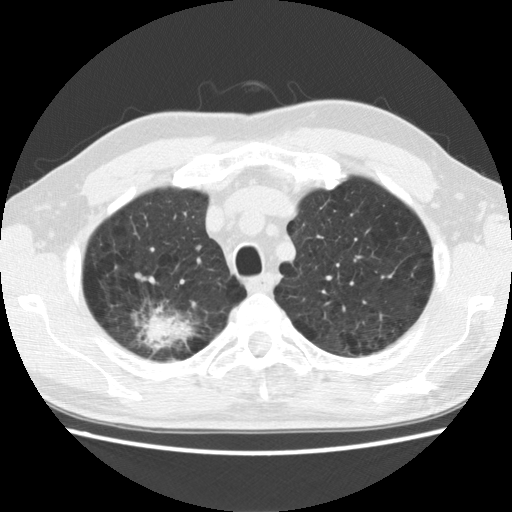
Low-dose screening chest CT, one axial slice. Slice 111 of 142 in the series (ordered by position). Lung window (W 1500 / L -600 HU). 512 × 512 image matrix, field of view 340 × 340 mm.
Outlined on this slice (expert manual segmentation):
- lesion 1 (tumor, upper lobe of right lung): bounding box (x1, y1, x2, y2) in pixels: (147, 318, 176, 344)